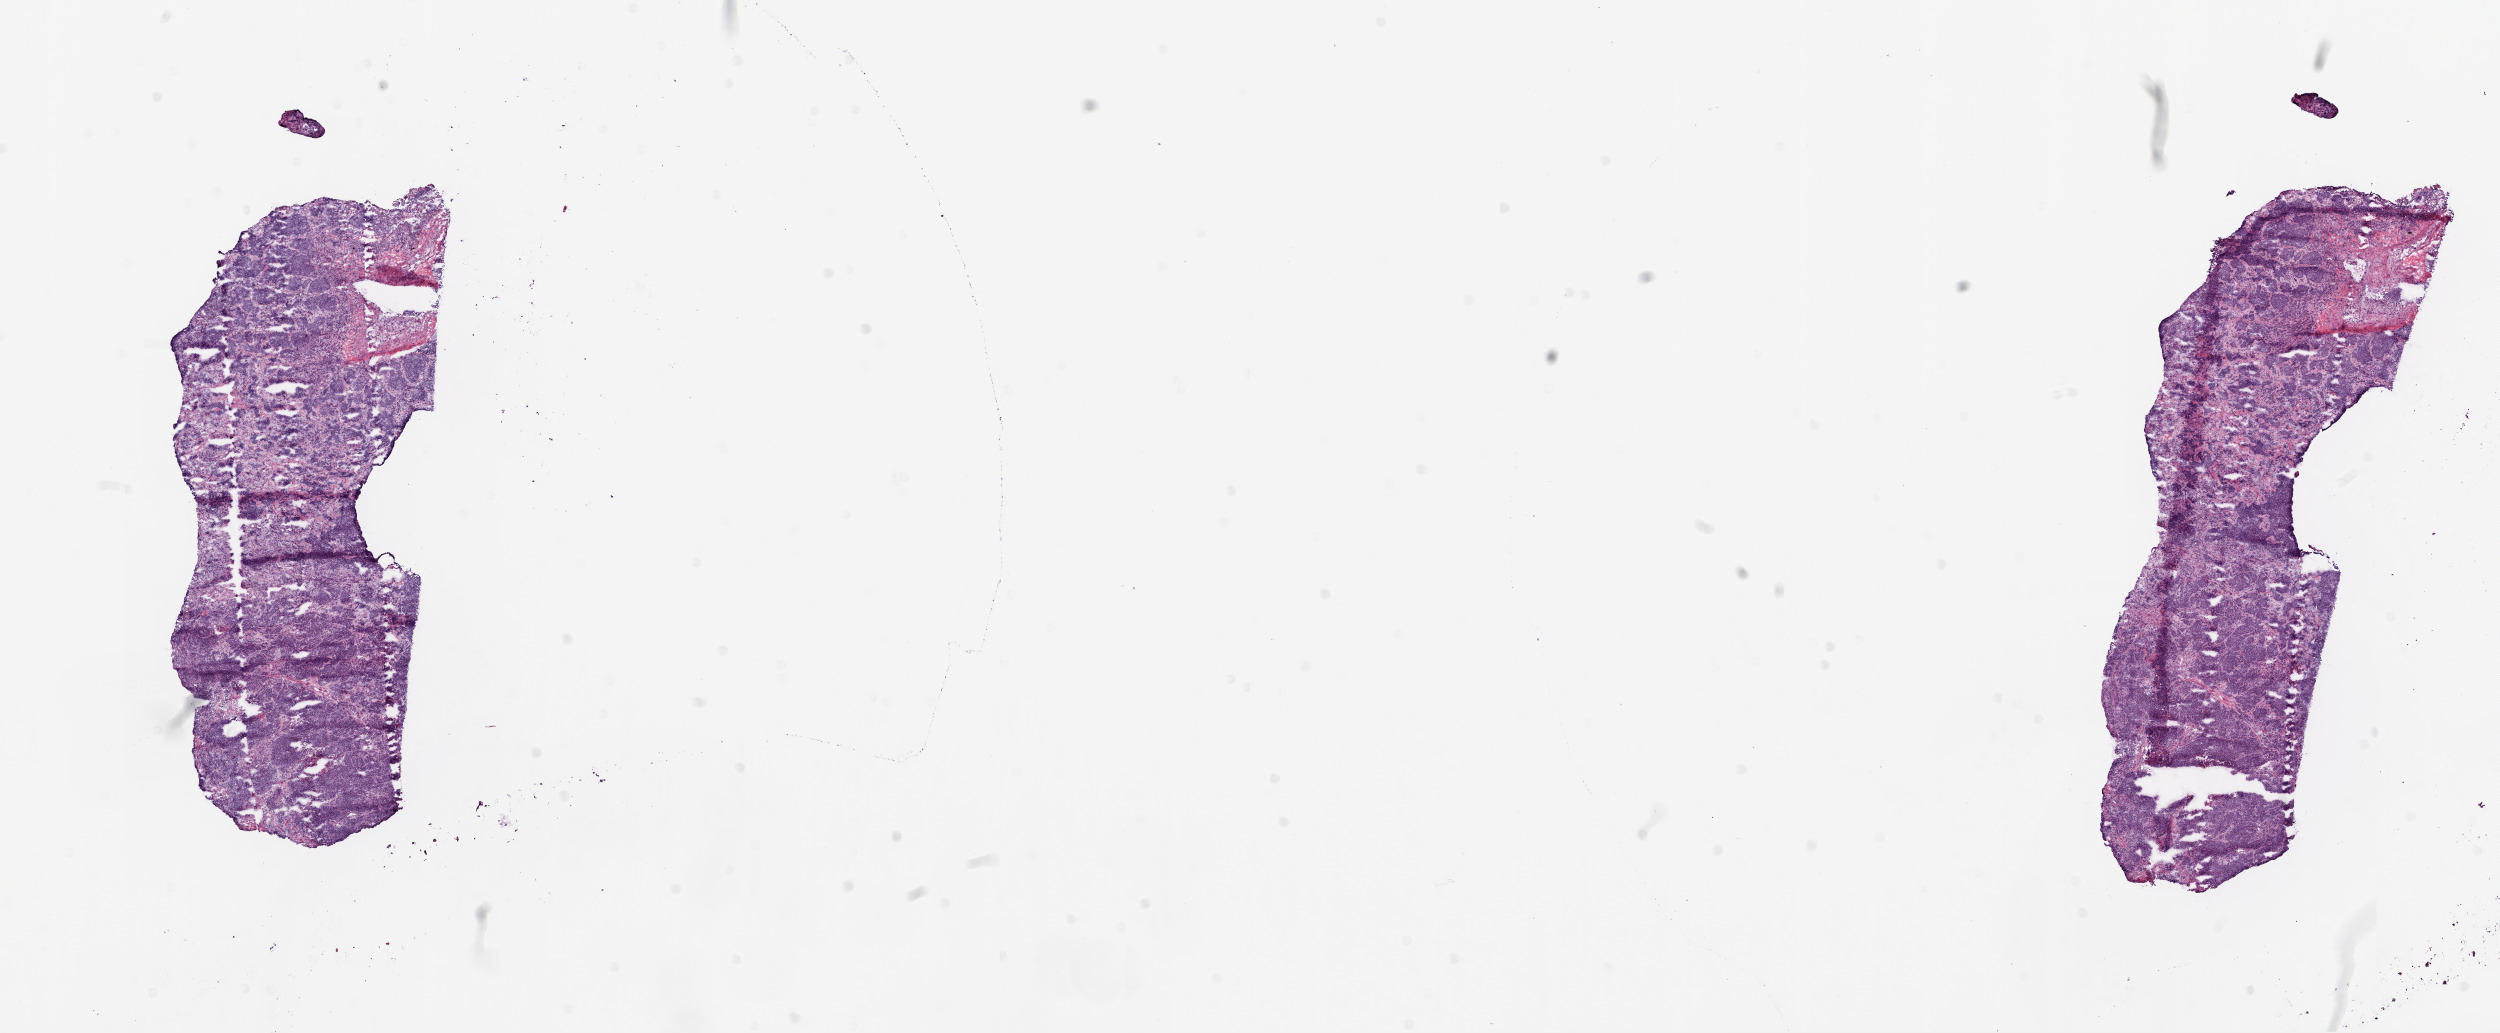
Digitized Hematoxylin and eosin (H&E) stained tissue section (whole slide) — low-resolution overview of the scanned area, about 20.1 x 8.3 mm (from a 20x scan); frozen section; lung, primary tumour sample. Female patient; age at initial diagnosis 65 years. Composition of this section per pathologist review: tumour cells 89%, tumour nuclei 90%, normal cells 0%, stromal cells 10%, necrosis 1%.
Pathologic diagnosis: Squamous cell carcinoma, NOS (upper lobe, lung). AJCC pathologic stage: IA (6th edition).